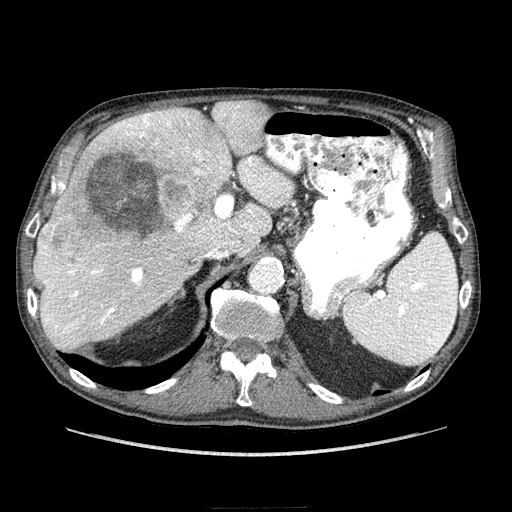
Contrast-enhanced abdominal CT (liver protocol), one axial slice; slice 157 of 218 in the series (ordered by position); reconstruction kernel STANDARD; 100 kVp; soft-tissue window (W 400 / L 40 HU); 2.5 mm slice thickness; 512 × 512 image matrix. From the clinical record (not read from this slice): diagnosis: hepatocellular carcinoma (patient treated with transarterial chemoembolisation; whether this scan precedes or follows treatment is not stated here); TNM stage (as recorded): Stage-IIIA; Child-Pugh class: A; tumour differentiation: well differentiated; tumour nodularity: multinodular.
Annotated regions visible in this slice (semi-automatic segmentation, software-assisted and operator-edited):
- liver parenchyma outside the tumour (the mass and vessels are separate outlines, so this box may not span the whole liver): box from (x=34, y=100) to (x=292, y=349) px
- mass: (x=47, y=107)–(x=233, y=261)
- liver vessels: (x=39, y=106)–(x=291, y=334)